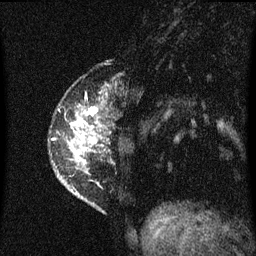
Breast MRI (dynamic contrast-enhanced), one sagittal slice; slice 14 of 60 in the series (ordered by position); dynamic contrast-enhanced series, image 2 of 3 at this slice position (ordered by acquisition); 1.5 T; TE 4.2 ms, TR 8.4 ms; 2 mm slice thickness; 256 × 256 image matrix, field of view 200 × 200 mm. Female patient, age 34 years. From the clinical record (not read from this slice): setting: breast cancer imaged before/during neoadjuvant chemotherapy; receptor status: HR-positive, HER2-negative.
Outlined on this slice (semi-automatic segmentation, software-assisted and operator-edited):
- analysis volume of interest (the breast-tissue region the enhancement analysis was run in; not a lesion): bounding box <62,108,103,199> (left, top, right, bottom; pixels)
- tumour enhancement mask (voxels above the 70 % enhancement threshold inside the analysis volume of interest): <88,110,95,115>